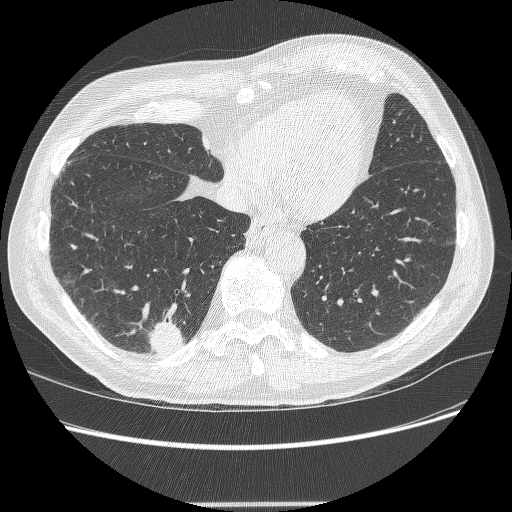
Axial slice from a low-dose chest CT screening exam. Second screening round (one year after baseline). Lung window (W 1500 / L -600 HU). 1.25 mm slice thickness. 120 kVp. Slice 66 of 245 in the series. Male participant, aged 71 years at enrolment. Current smoker at enrolment.
• Expert-annotated lung lesion, bounding box [x1, y1, x2, y2] px = [137, 322, 188, 361].
• The screening reader recorded 5 non-calcified nodules or masses ≥4 mm on this exam (right lower lobe, right lower lobe, right upper lobe, right upper lobe, right upper lobe); which of them this box marks is not recorded.
• Participant outcome: lung cancer diagnosed 7 days after this screen — squamous cell carcinoma, NOS, right lower lobe, moderately differentiated (G2), stage IA (AJCC 6th edition), 27 mm at pathology.